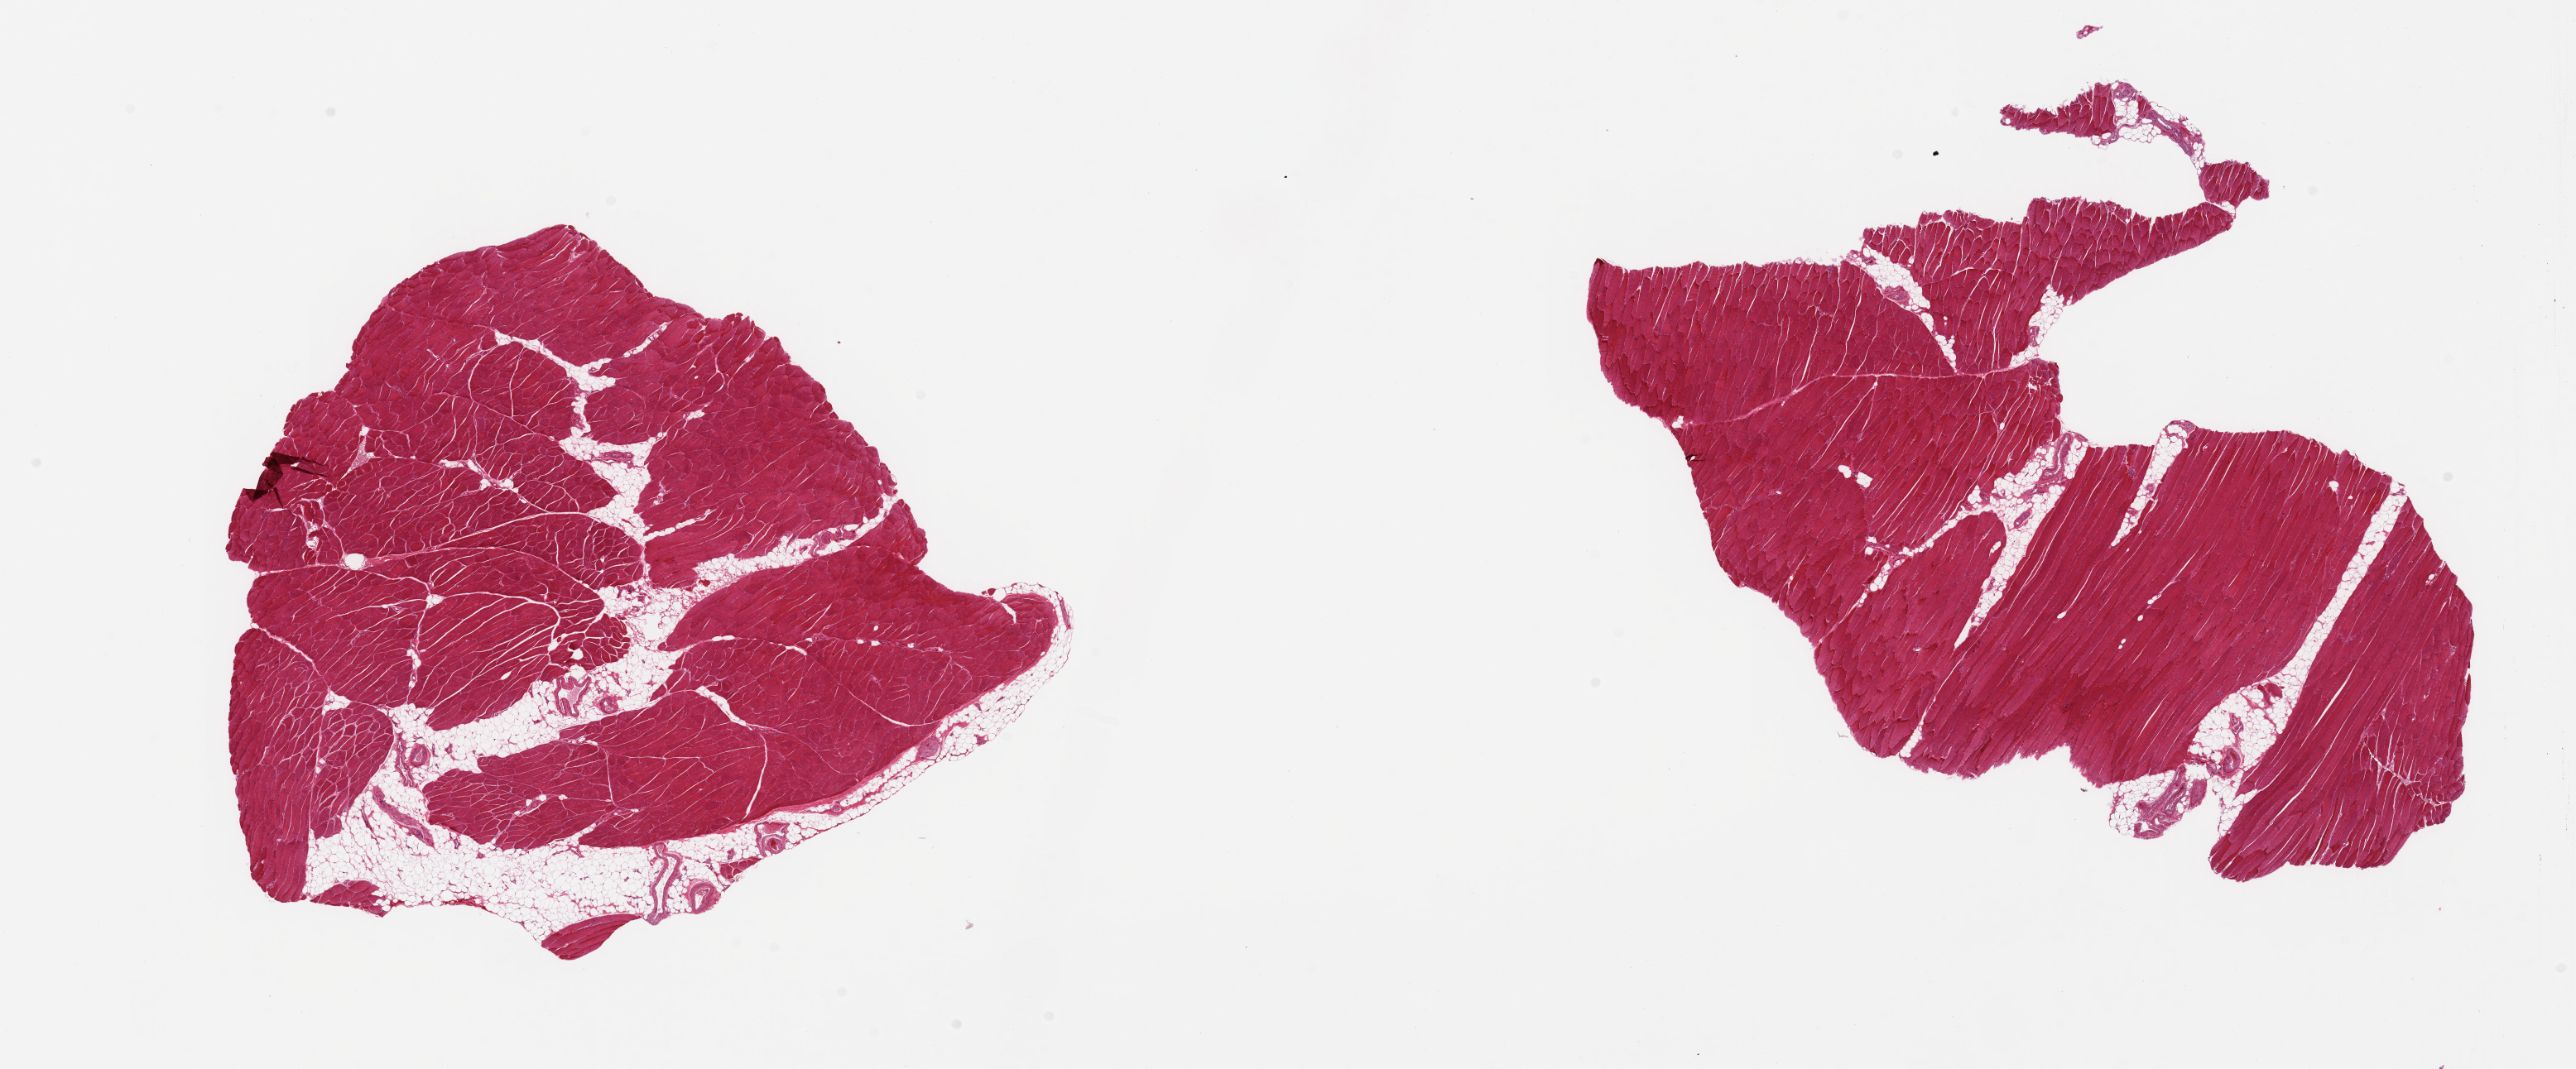
Digitized hematoxylin and eosin (H&E)-stained section, brightfield — shown as a low-resolution overview of the whole scanned area (about 24.6 x 10.2 mm, acquisition: 20x scan). PAXgene-fixed, paraffin-embedded tissue. Section of skeletal muscle (target tissue). Donor tissue sample. Donor: male.
Reviewer comment on this tissue sample: 2 pieces, interstitial/adherent fat/vascular elements are ~10% of tissue.